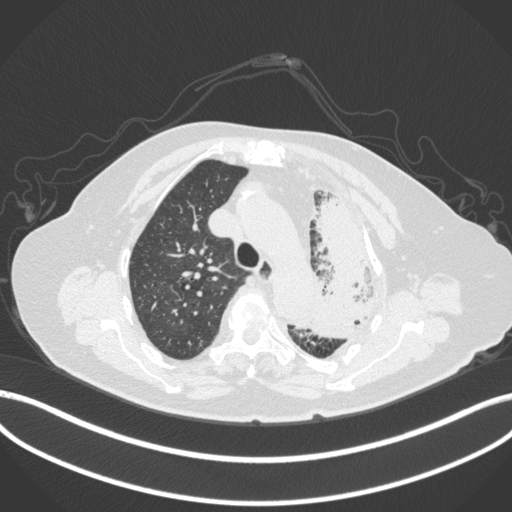
Chest CT, one axial slice. Slice 293 of 399 in the series (ordered by position). Reconstruction kernel B31f. 120 kVp. Lung window (W 1500 / L -600 HU). 512 × 512 image matrix. Female patient, age 75 years. Case-level facts recorded for this patient, not image findings: clinical TNM (as recorded): T3 N3 M1.
Annotated regions visible in this slice (bounding box drawn by a radiologist):
- lung tumour (recorded histology: adenocarcinoma): bounding box [x1, y1, x2, y2] px = [298, 193, 384, 343]